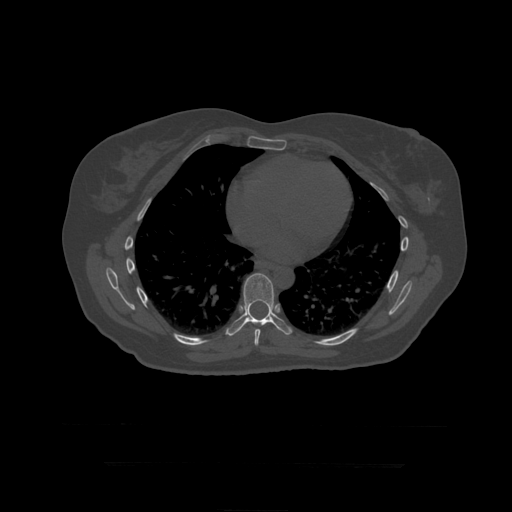
CT including the spine, one axial slice; position 267 of 399 along the scan axis; reconstruction kernel STANDARD; bone window (W 1800 / L 400 HU); 1.25 mm slice thickness; 512 × 512 image matrix, field of view 450 × 450 mm. Patient age 41 years. From the clinical record (not read from this slice): primary cancer: breast.
Annotated regions visible in this slice (semi-automatically segmented with operator editing):
- T8 vertebra: box from (x=254, y=329) to (x=261, y=346) px
- T9 vertebra: (x=226, y=273)–(x=292, y=336)